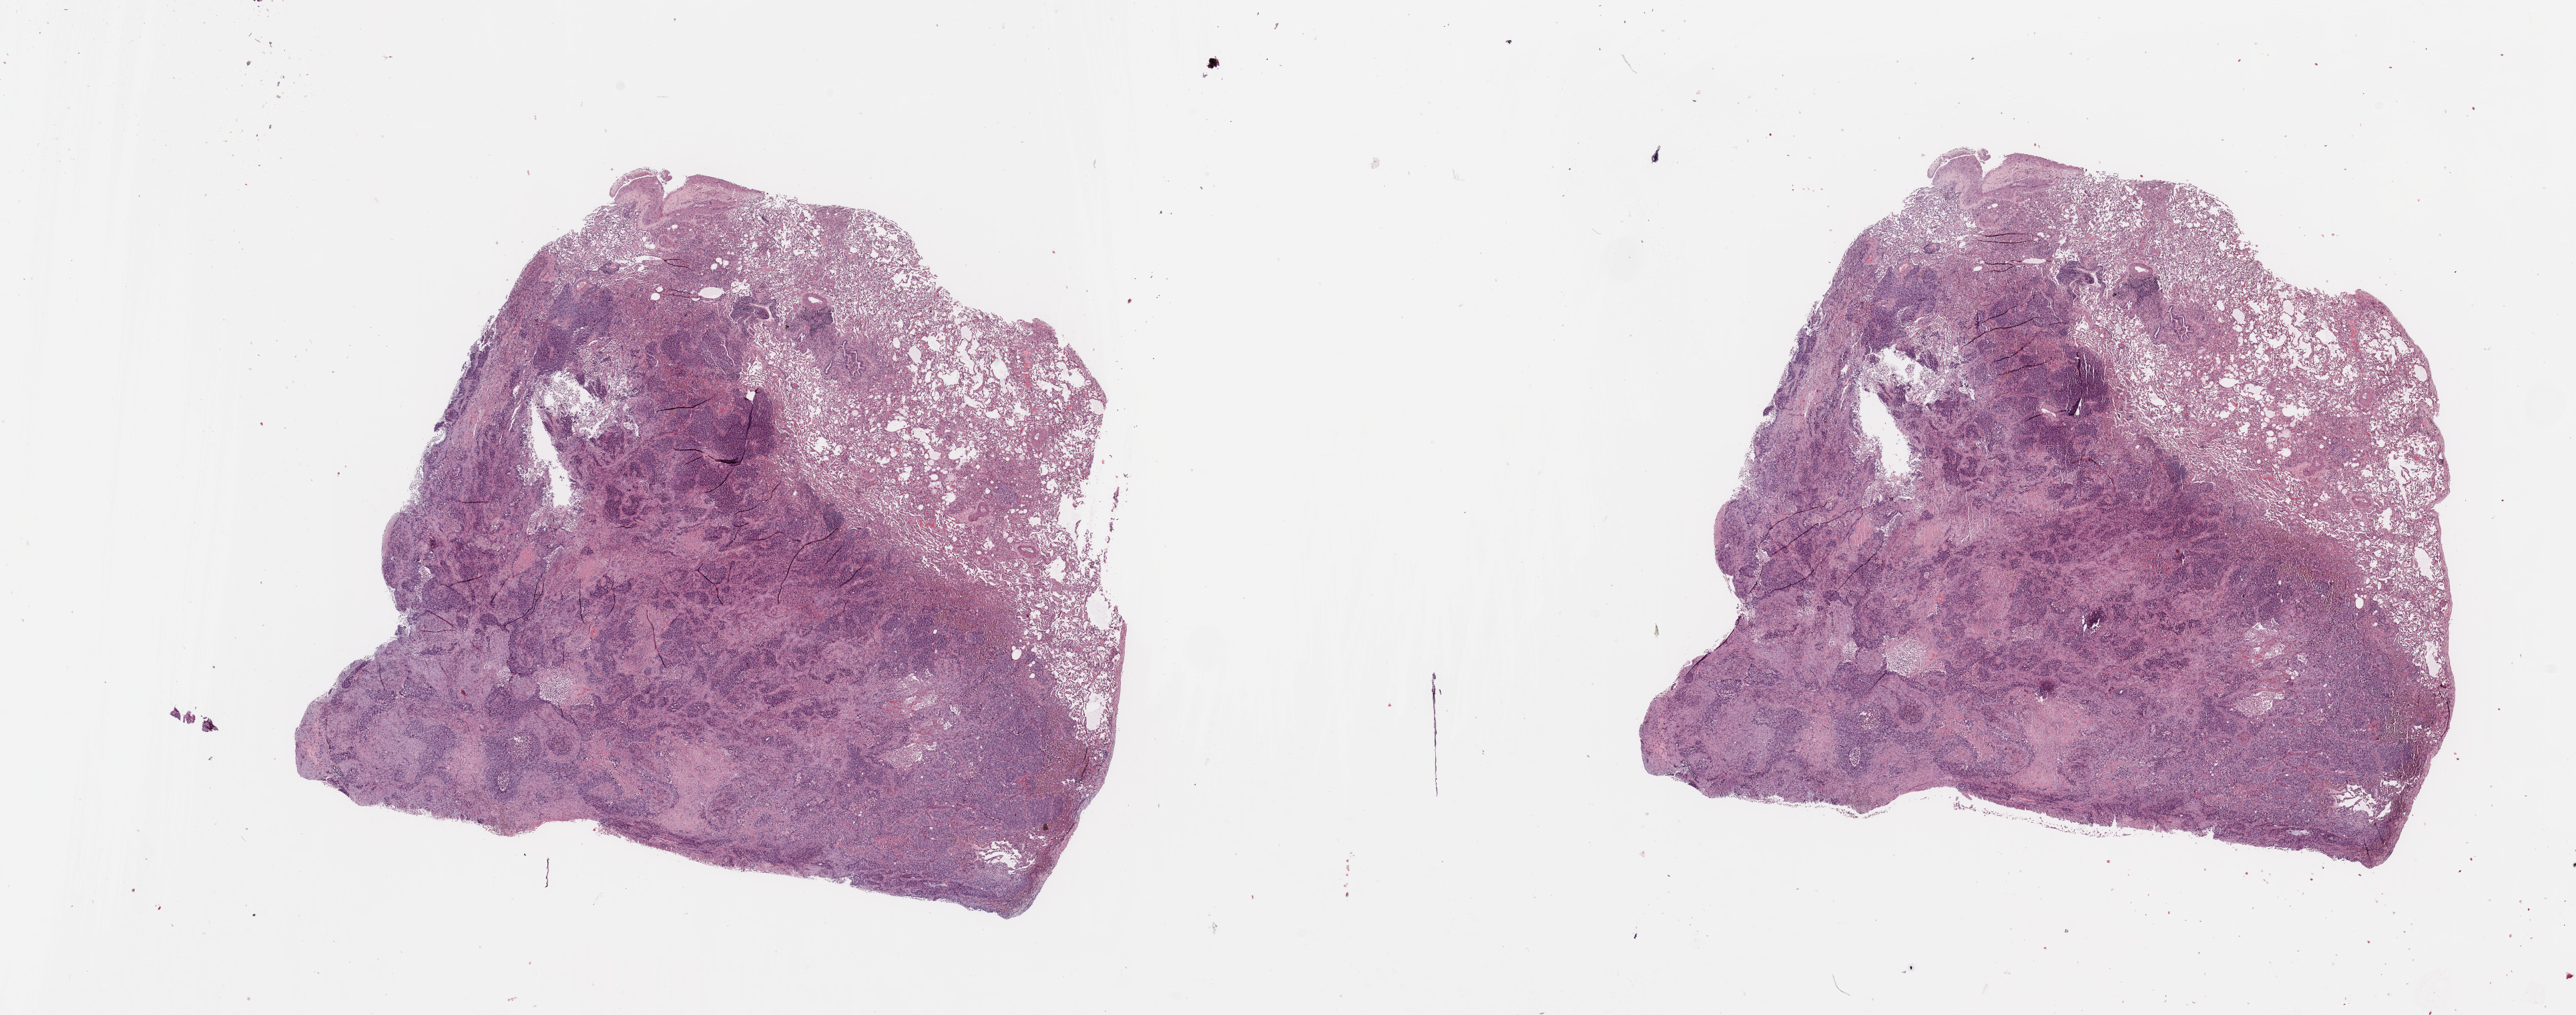
Whole-slide histology image, Hematoxylin and eosin (H&E) stained — low-resolution overview of the scanned area, about 30.5 x 12.0 mm (acquisition: 20x scan), tumour tissue sample, lung. Patient: male, age 57 years. Histologic grade: G3 (poorly differentiated).
- primary tumour site (as recorded): right lower lobe
- histologic diagnosis: Squamous cell carcinoma, NOS
- AJCC pathologic stage: IA